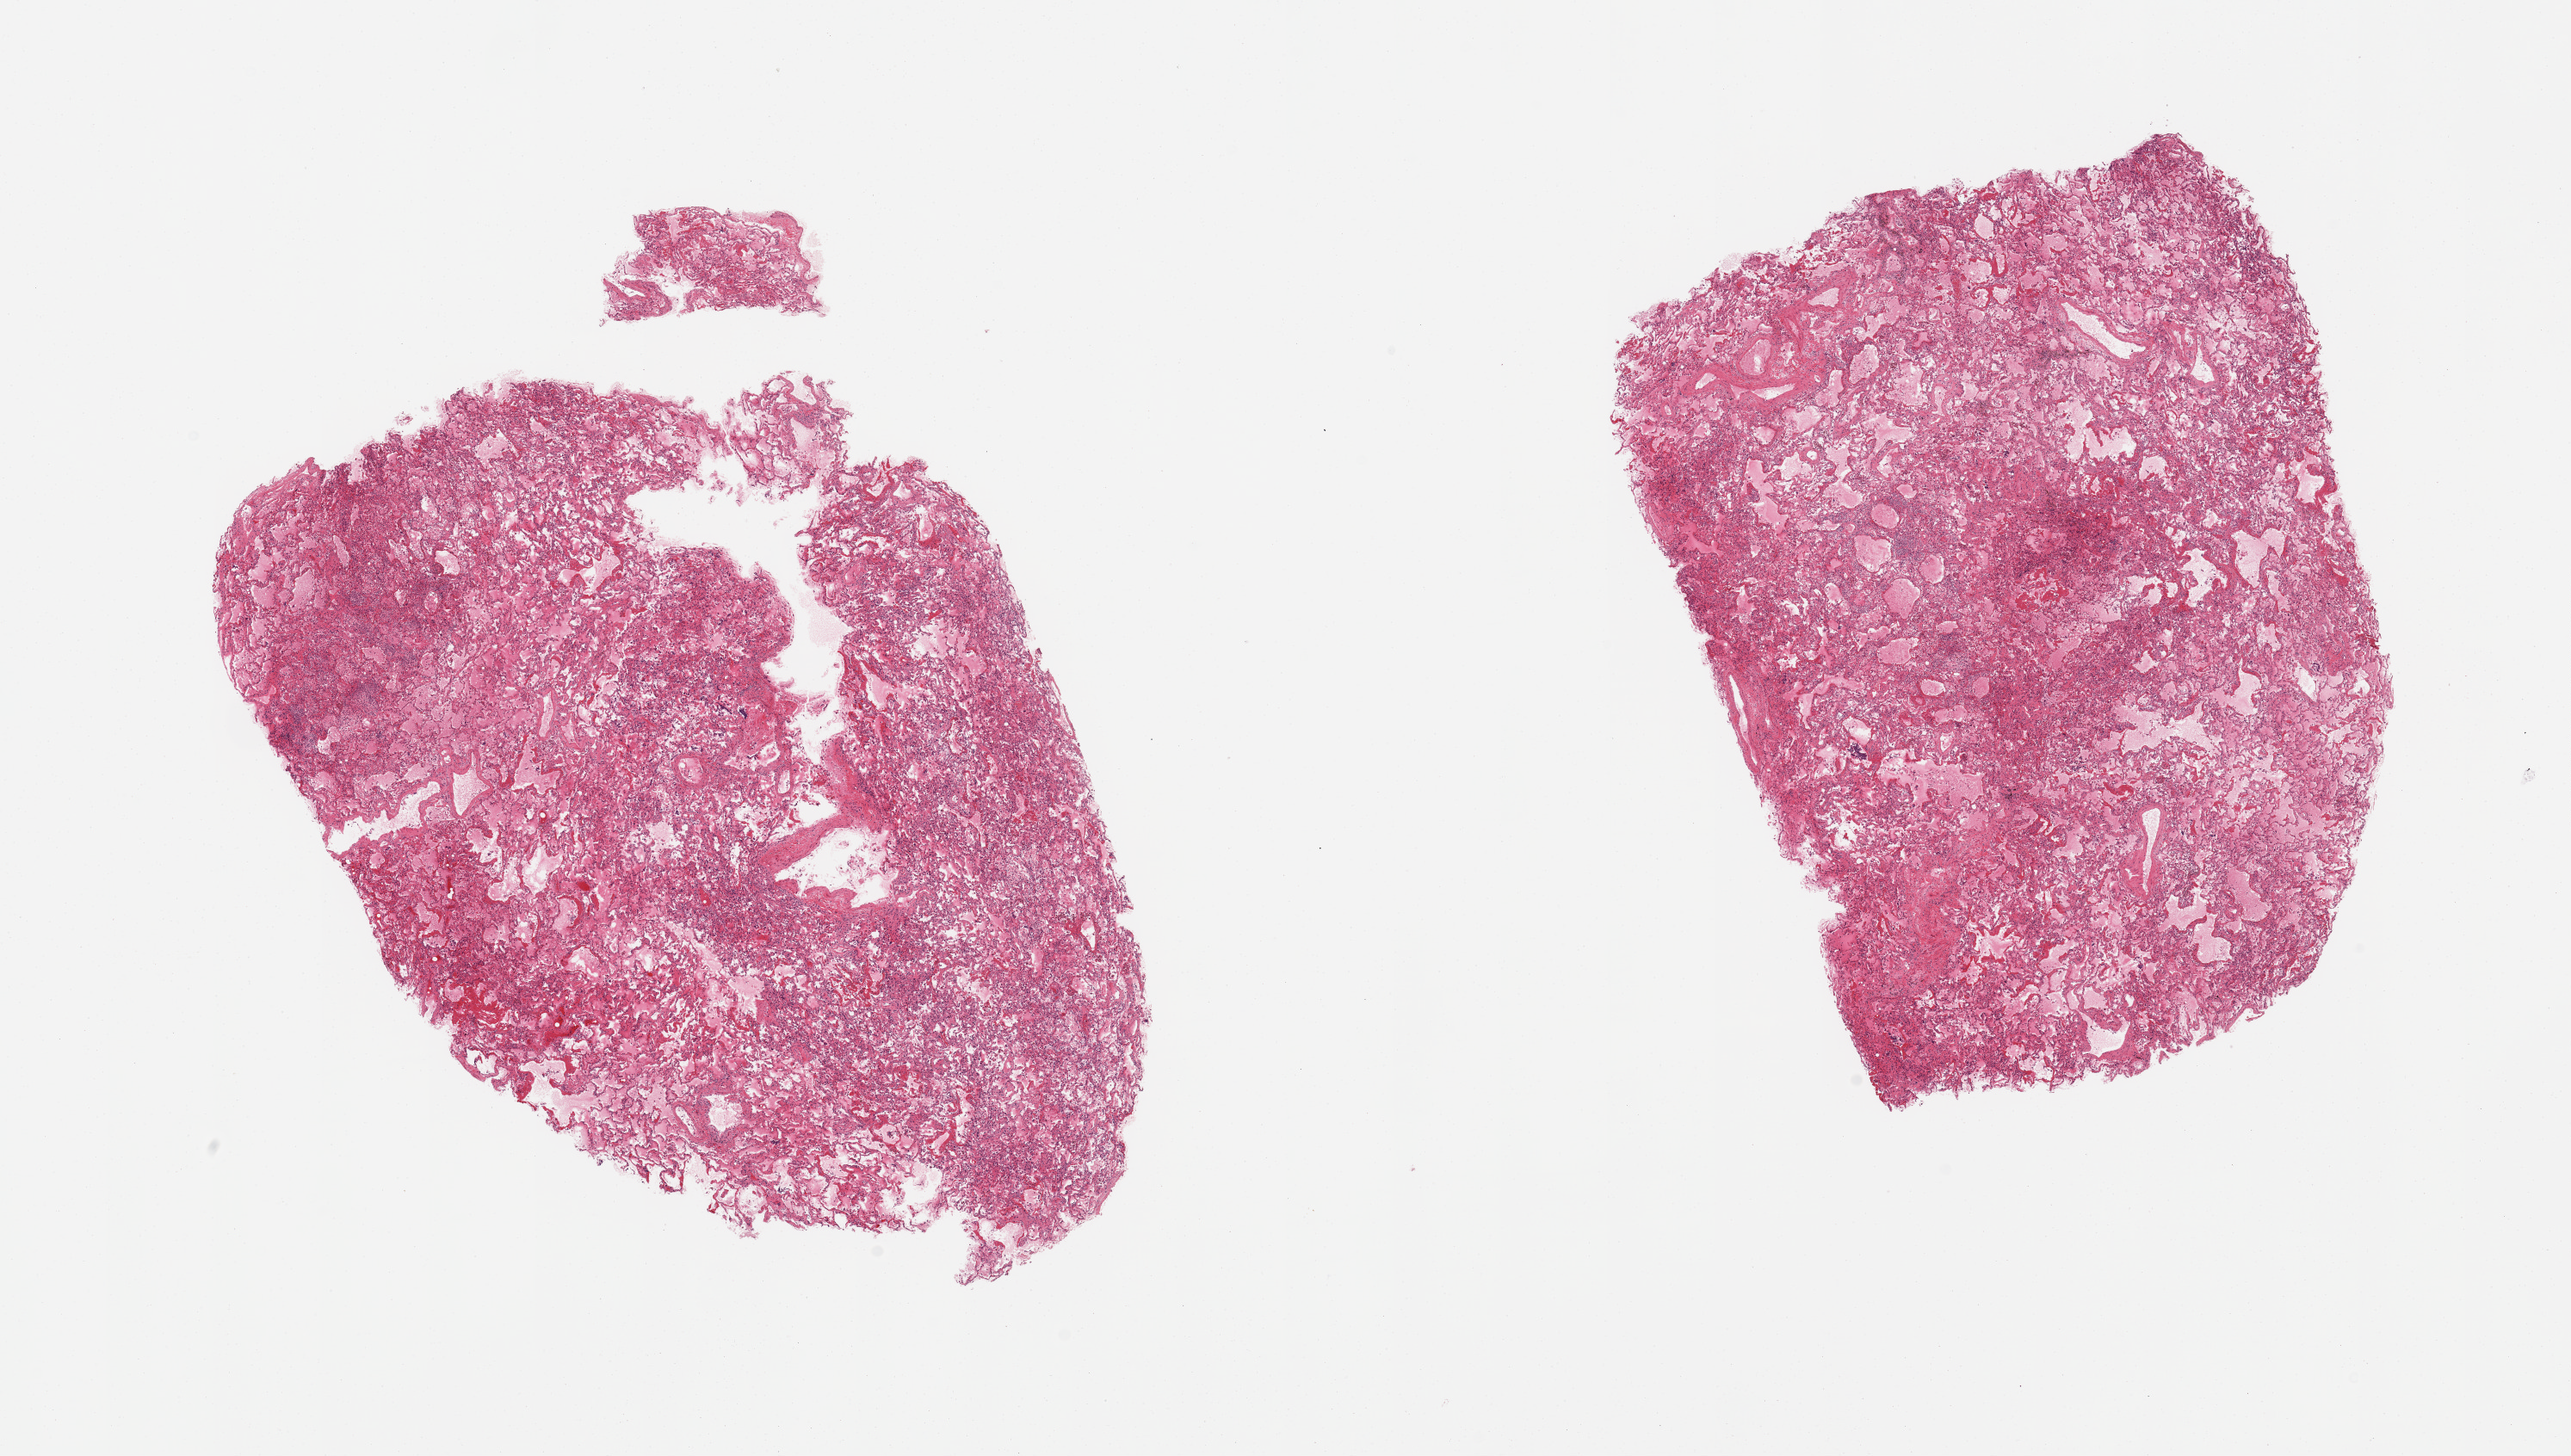
Hematoxylin and eosin (H&E) whole-slide image — shown as a low-resolution overview of the whole scanned area (about 23.6 x 13.4 mm), PAXgene-fixed, paraffin-embedded tissue, section of lung (target tissue), tissue donor sample. Donor: female.
- review note (as recorded): 2 pieces; congestion, edema, fibrin, patchy pneumonia